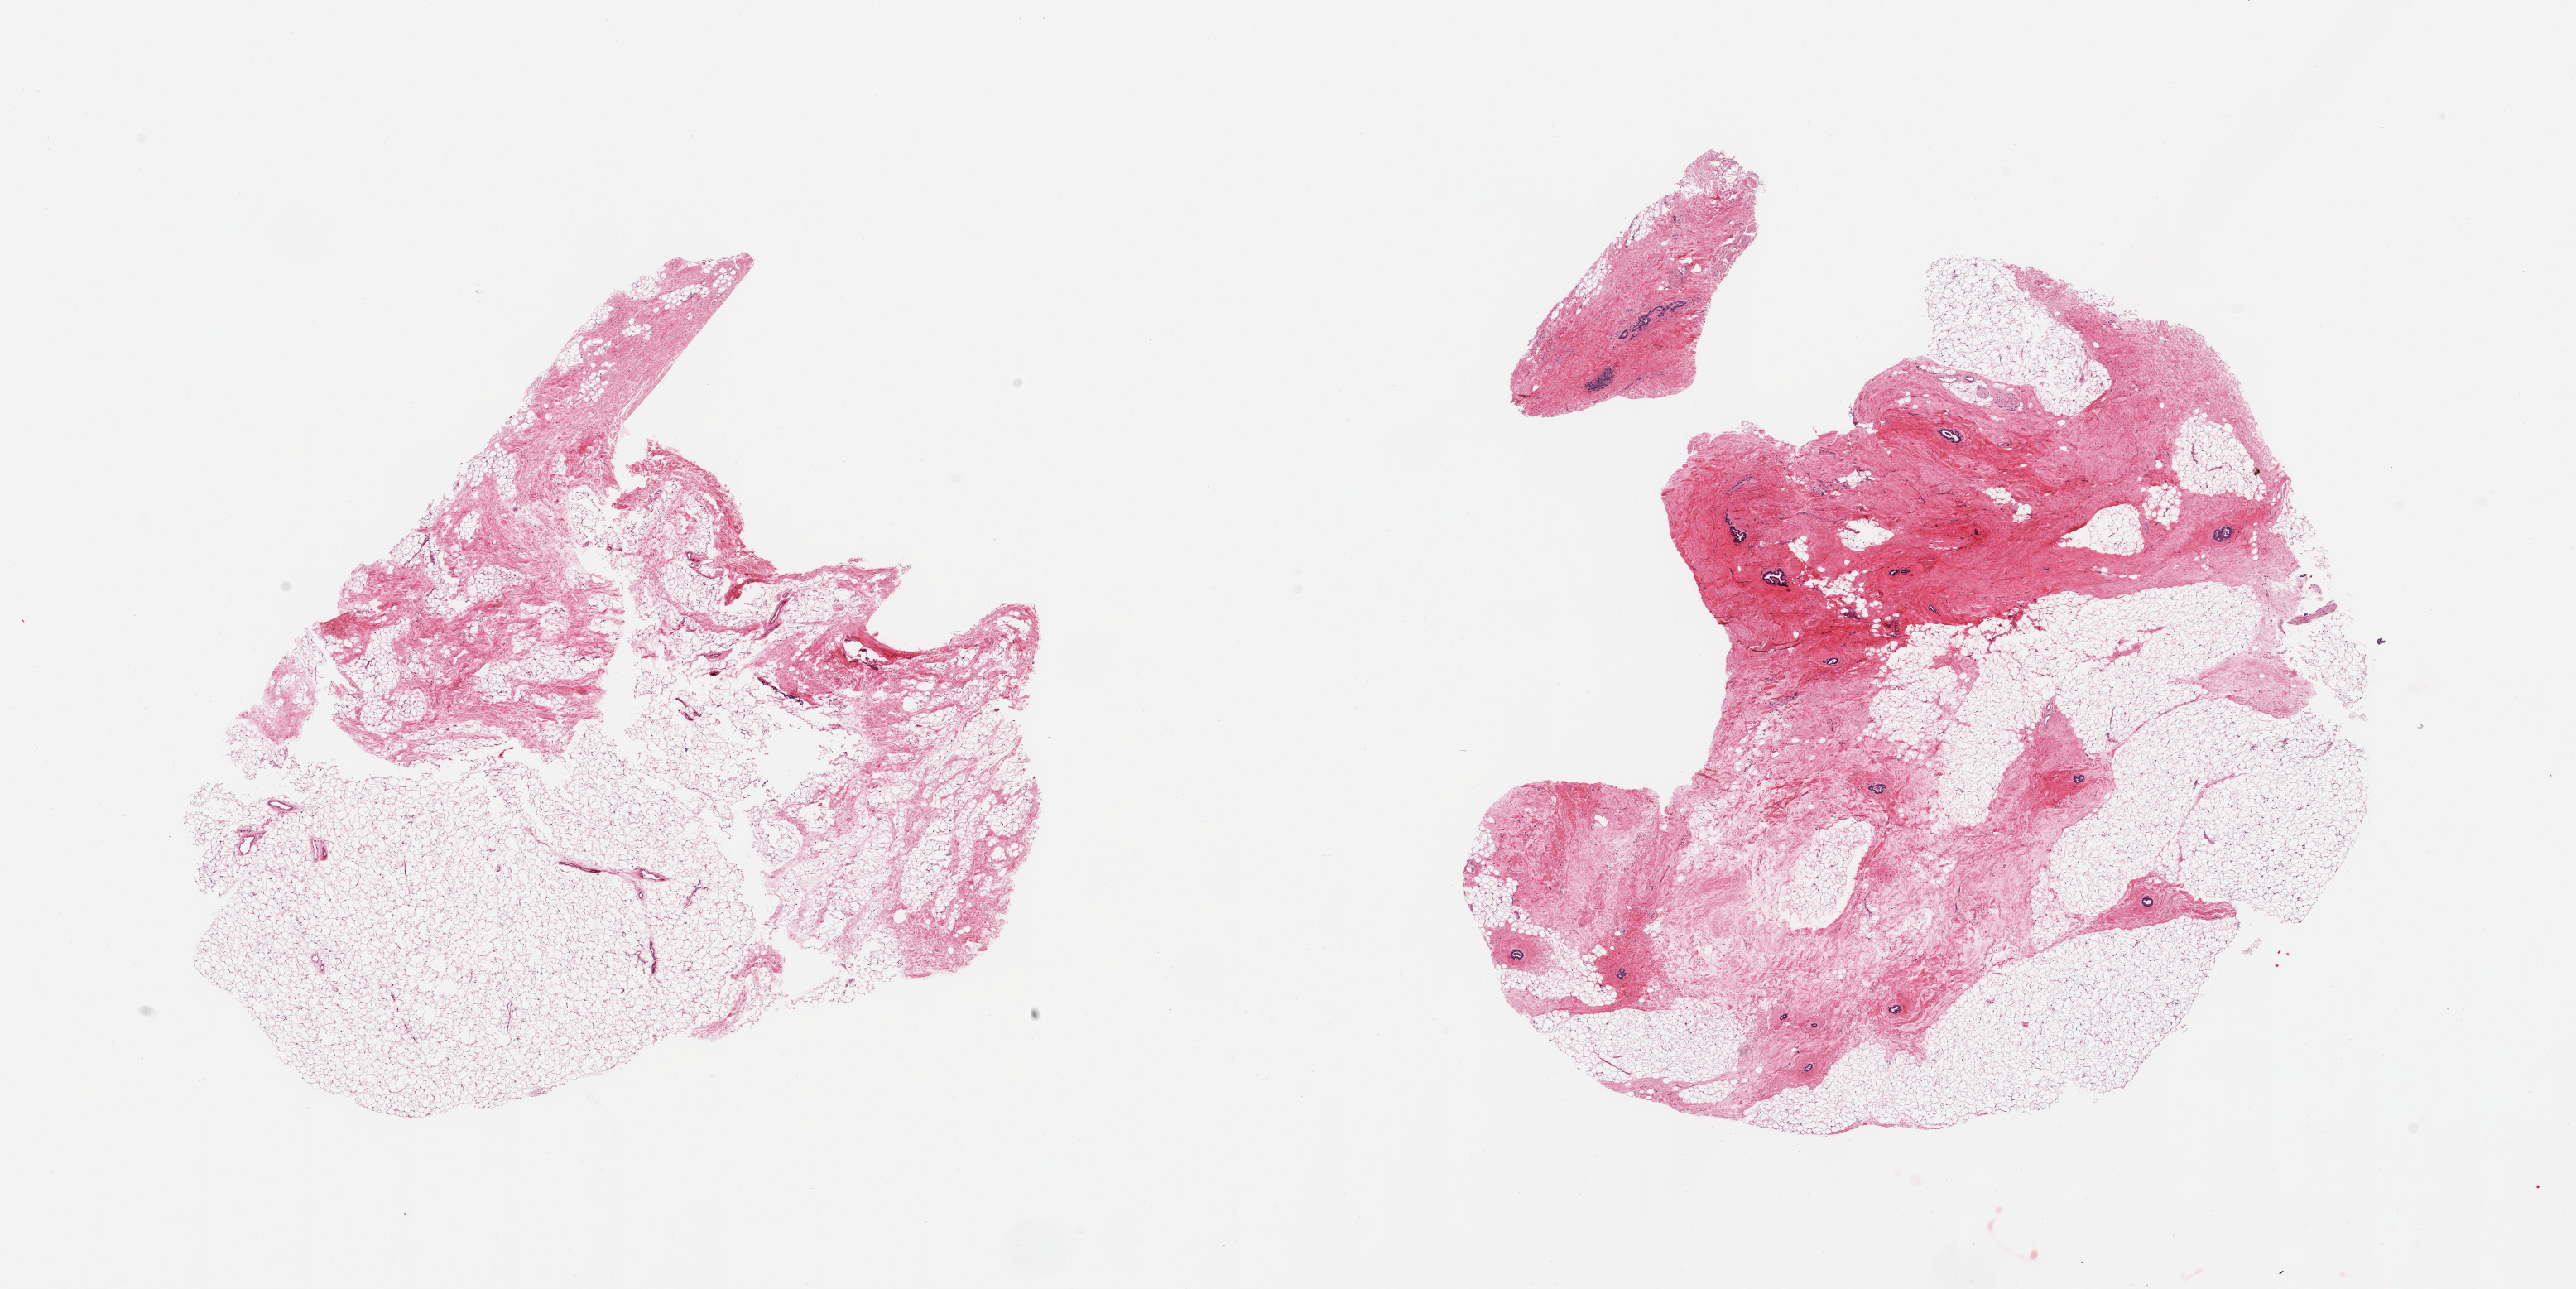
Haematoxylin and eosin whole-slide image — shown as a low-resolution overview of the whole scanned area (about 24.6 x 12.3 mm, slide scanned at 20x). PAXgene-fixed paraffin-embedded (PFPE) section. Target tissue: breast. Donor tissue sample. Donor sex: male.
Review note (as recorded): 2 pieces; one consists of 60% mature adipose tissue/40% fibrous tissue, other 40% mature adipose tissue/60% ductal structures embedded in fibrous stroma.